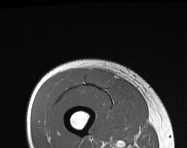
MRI of an extremity soft-tissue mass, one axial slice; slice 38 of 114 in the series (ordered by position); MR volume resampled by the dataset authors to the PET/CT grid (not the native acquisition matrix); 3.27 mm slice thickness; 187 × 148 image matrix. Male patient. From the clinical record (not read from this slice): histological type: pleiomorphic leiomyosarcoma; grade: intermediate; site of the primary tumour: right thigh.
Structures marked on this image (expert contour drawn on MRI and transferred to this co-registered scan by the dataset authors):
- gross tumour volume including surrounding oedema: bounding box <86,70,113,87> (left, top, right, bottom; pixels)